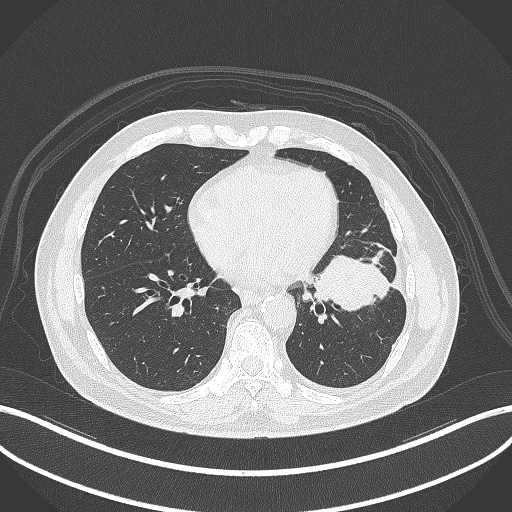
Chest CT, one axial slice. Slice 140 of 230 in the series (ordered by position). Reconstruction kernel B70f. 120 kVp. Lung window (W 1500 / L -600 HU). 1 mm slice thickness. 512 × 512 image matrix. Male patient, age 68 years. From the clinical record (not read from this slice): clinical TNM (as recorded): T2b N0 M0.
Annotated regions visible in this slice (rectangle marked by the reading radiologist):
- lung tumour (recorded histology: squamous cell carcinoma): bounding box <309,251,393,314> (left, top, right, bottom; pixels)